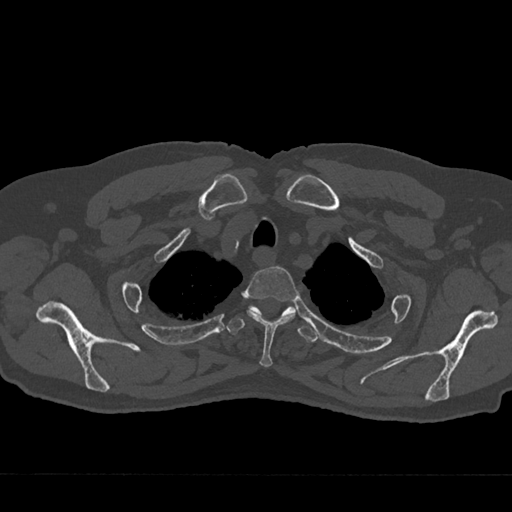
CT including the spine, one axial slice. Slice 596 of 797 in the series (ordered by position). Reconstruction kernel Br40s/3. 120 kVp. Bone window (W 1800 / L 400 HU). 0.5 mm slice thickness. 512 × 512 image matrix, field of view 377 × 377 mm. Male patient, age 75 years. Case-level facts recorded for this patient, not image findings: primary cancer: renal; vertebrae with lytic lesions (as recorded): T4.
Outlined on this slice (semi-automatically segmented with operator editing):
- T2 vertebra: box from (x=242, y=266) to (x=299, y=368) px
- T3 vertebra: (x=226, y=306)–(x=318, y=342)